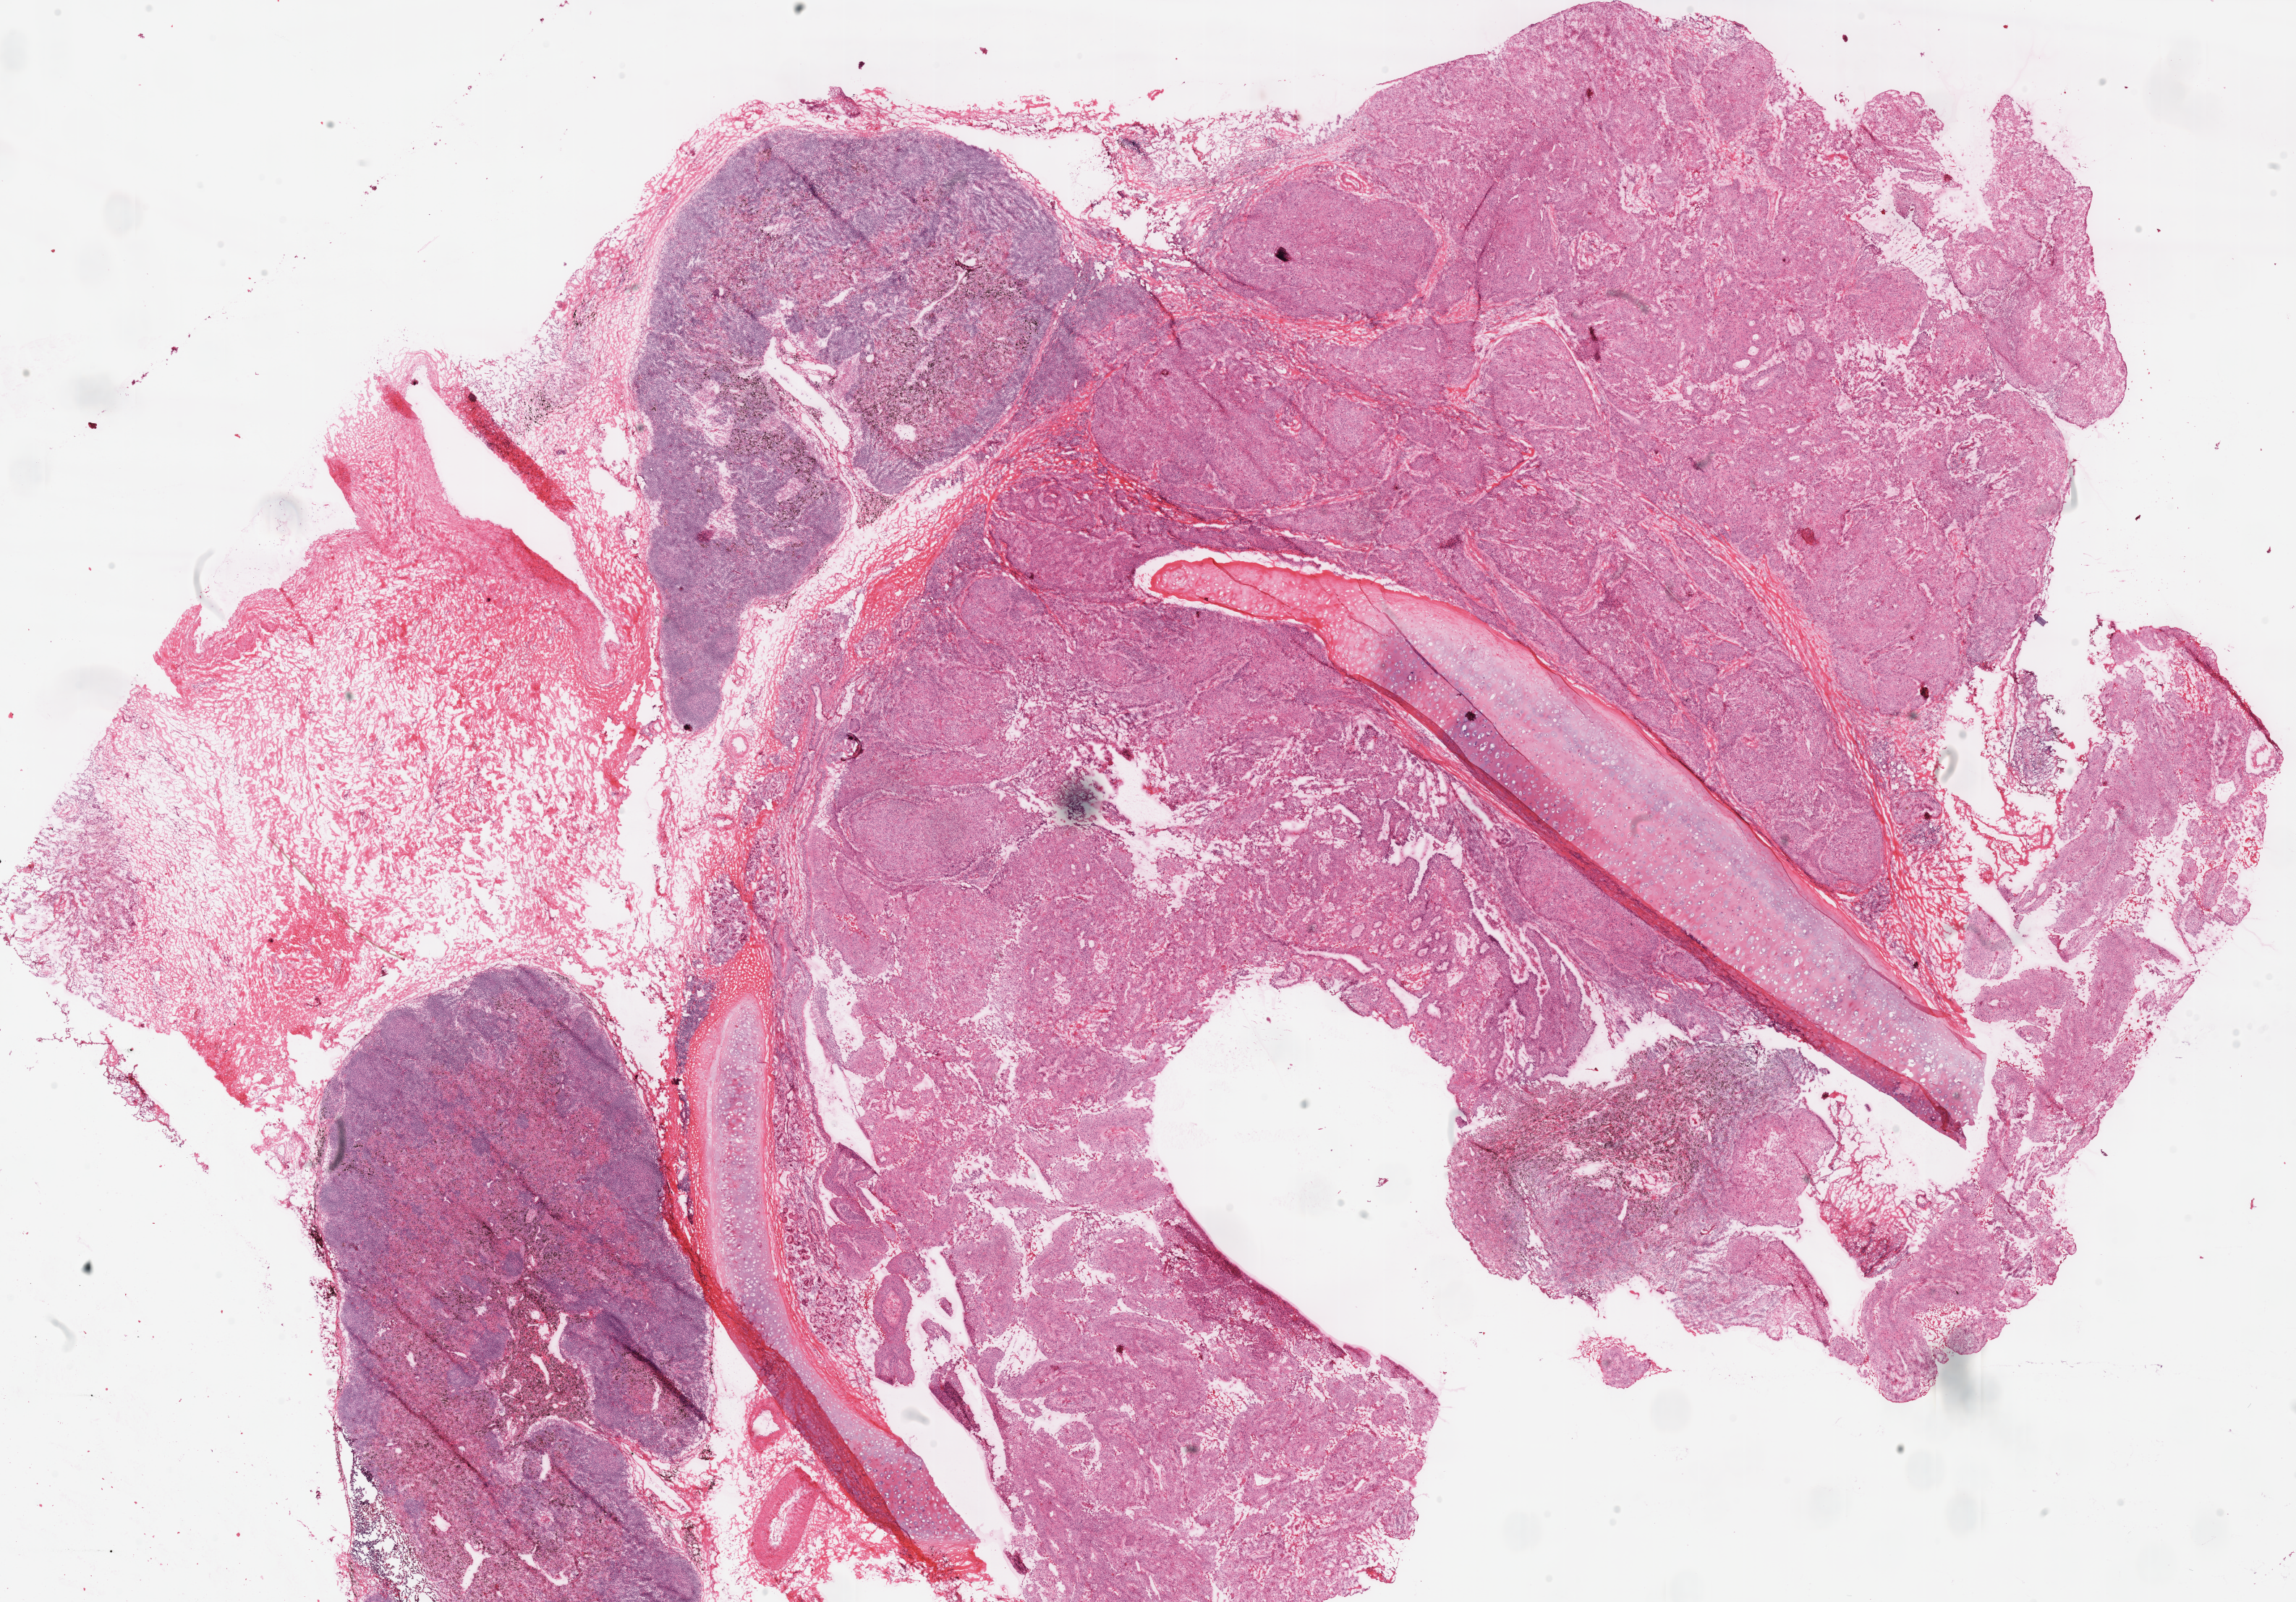
H&E whole-slide image, whole scanned area (about 25.0 x 17.4 mm) shown as a low-resolution overview; frozen section; primary tumour sample from the lung. Male patient; age at initial diagnosis 63 years. Composition of this section per pathologist review: tumour cells 60%, tumour nuclei 70%, normal cells 0%, stromal cells 25%, necrosis 15%.
Diagnosis: Squamous cell carcinoma, NOS (upper lobe, lung). Laterality: left. TNM: T1a N0 M0. AJCC pathologic stage: IA (7th edition).